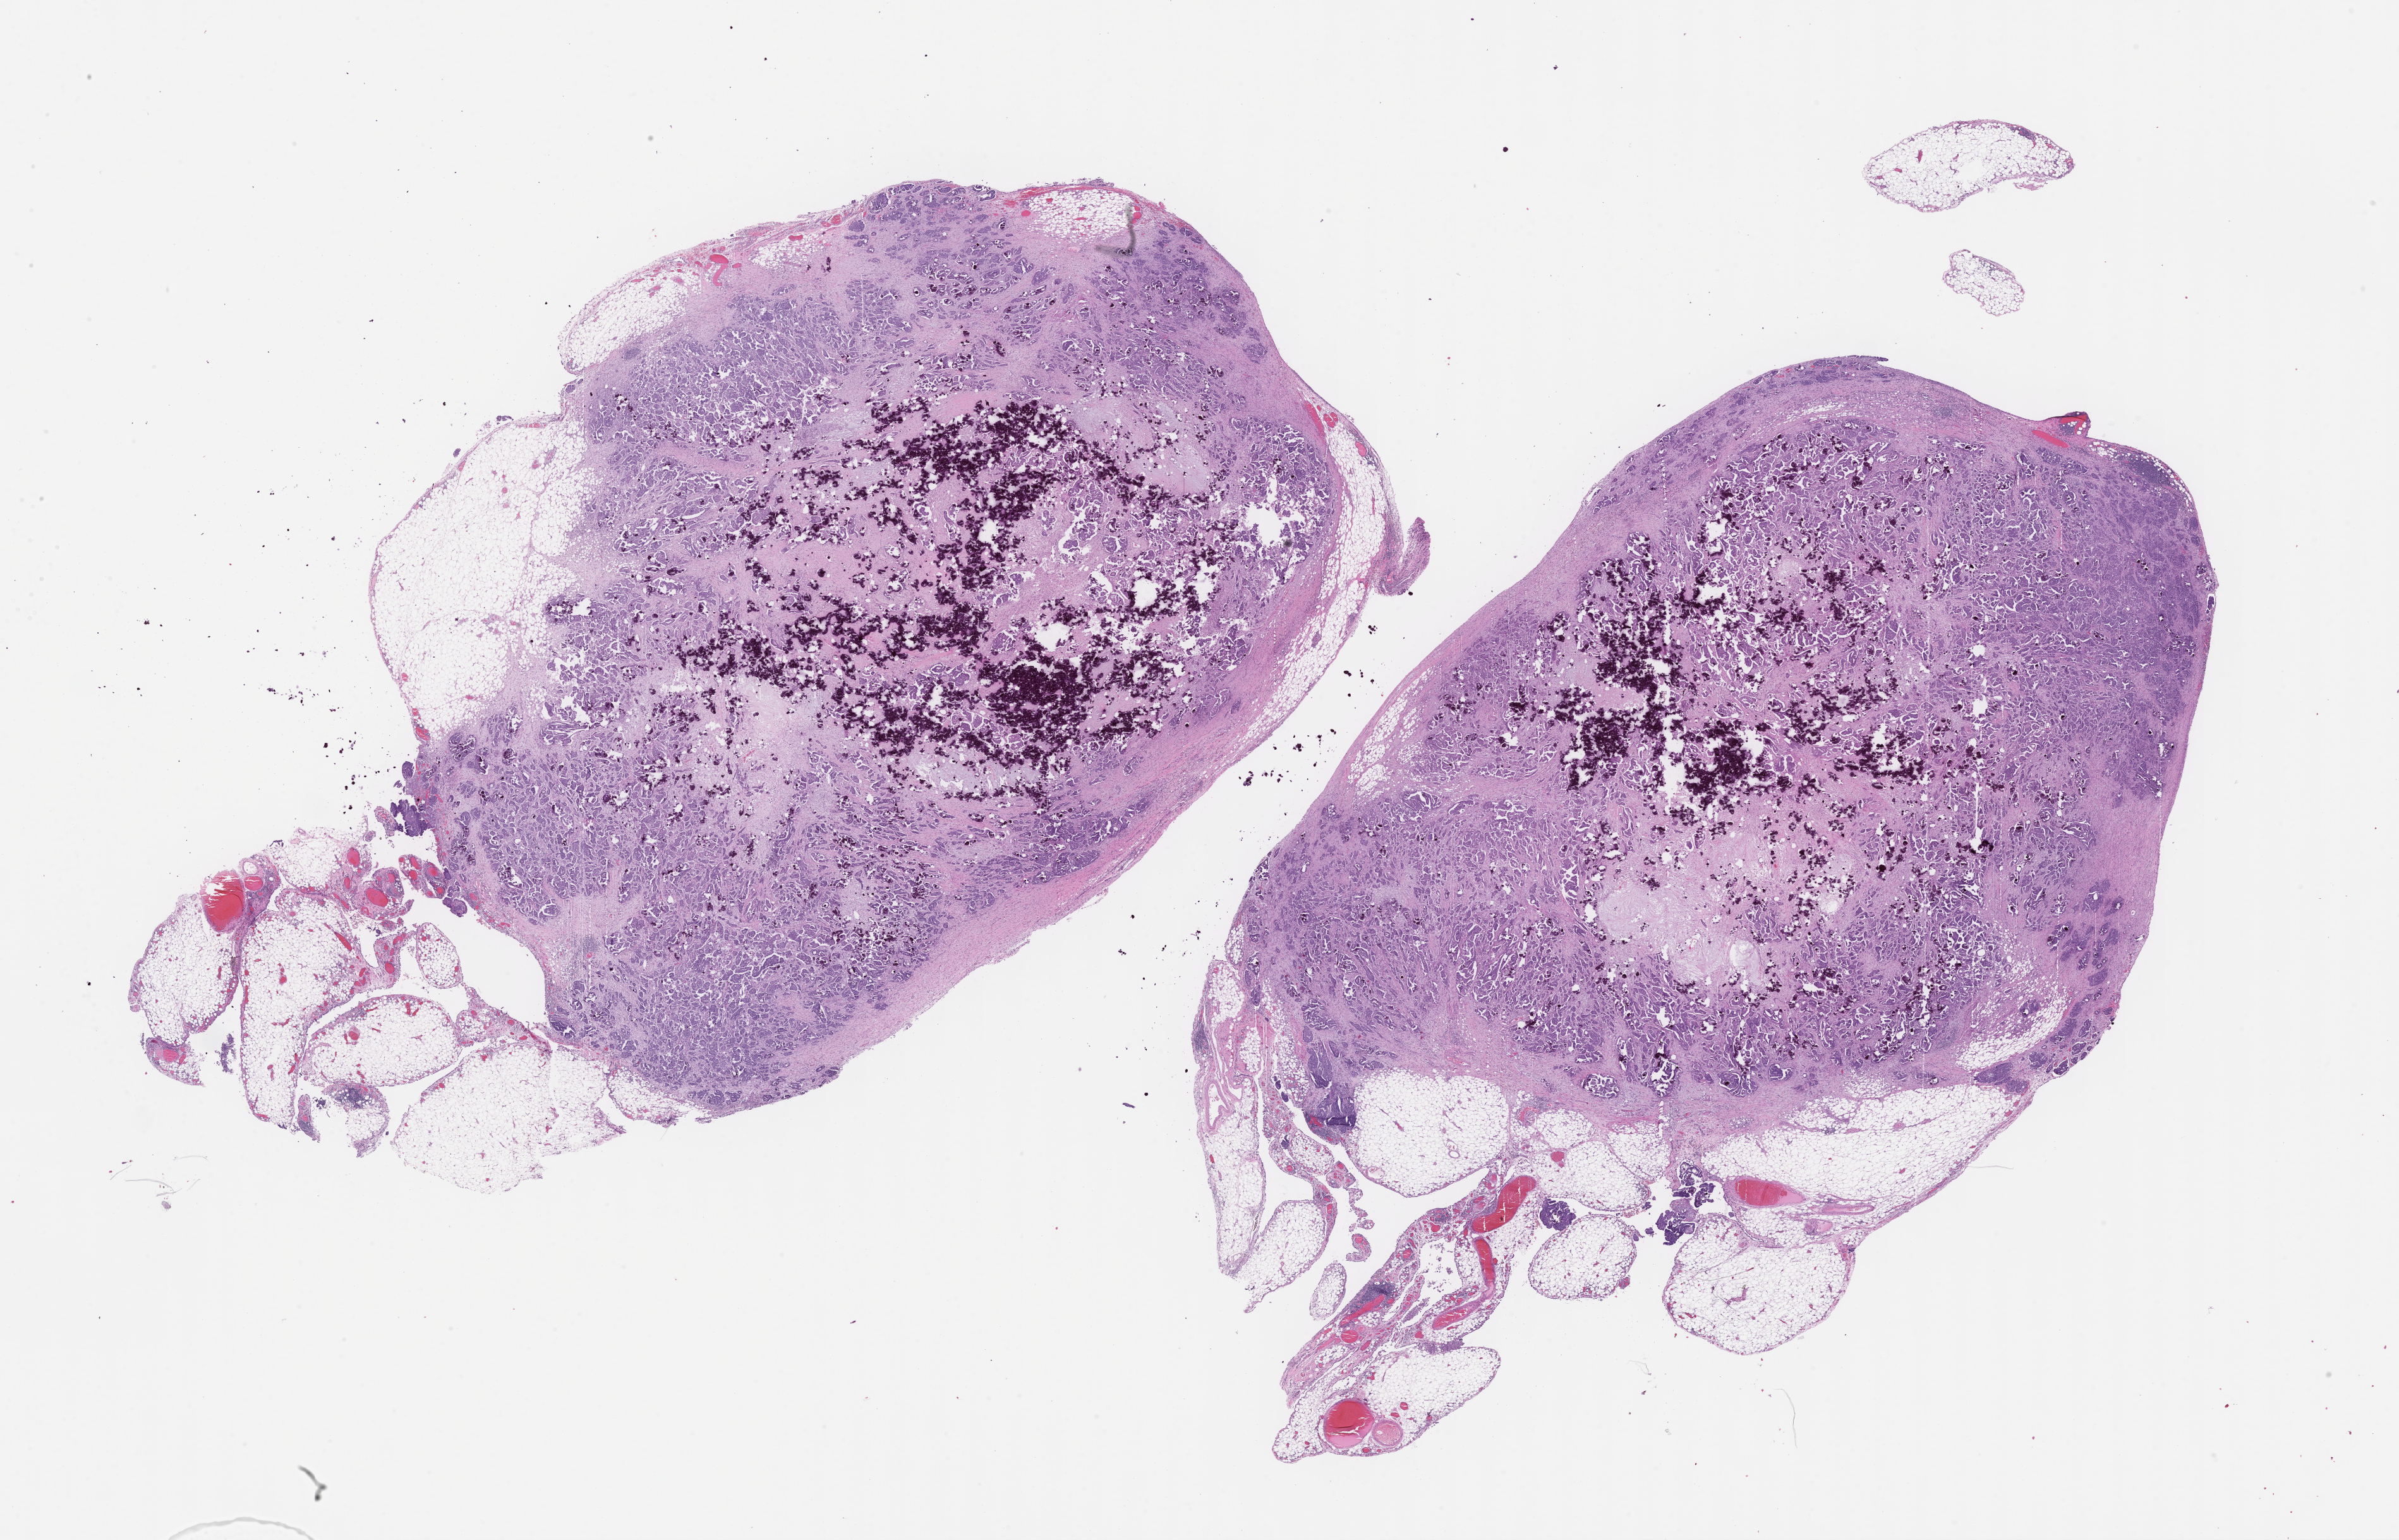
Hematoxylin and eosin (H&E) whole-slide image, a low-resolution overview of the entire scanned area, about 30.7 x 19.7 mm; formalin-fixed, paraffin-embedded (FFPE) tissue; site: omentum. Female patient.
- this section: primary tumour tissue
- diagnosis: Fallopian Tube Carcinoma